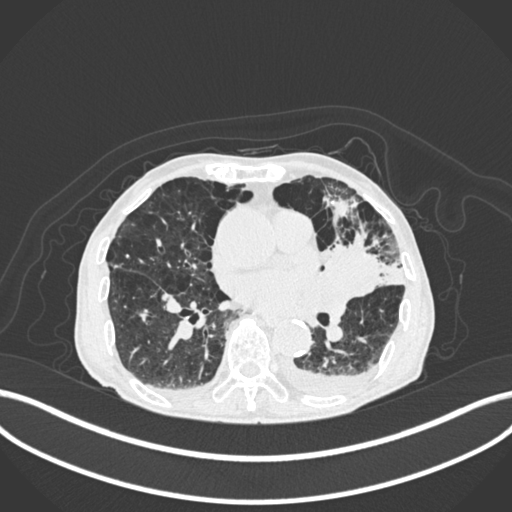
Chest CT, one axial slice; position 98 of 400 along the scan axis; reconstruction kernel B30f; 120 kVp; lung window (W 1500 / L -600 HU); 1 mm slice thickness; 512 × 512 image matrix. Patient: male, 90 years or older. Case-level facts recorded for this patient, not image findings: clinical TNM (as recorded): T2b N1 M0.
Outlined on this slice (rectangle marked by the reading radiologist):
- lung tumour (recorded histology: squamous cell carcinoma): bounding box [x1, y1, x2, y2] px = [325, 236, 383, 302]